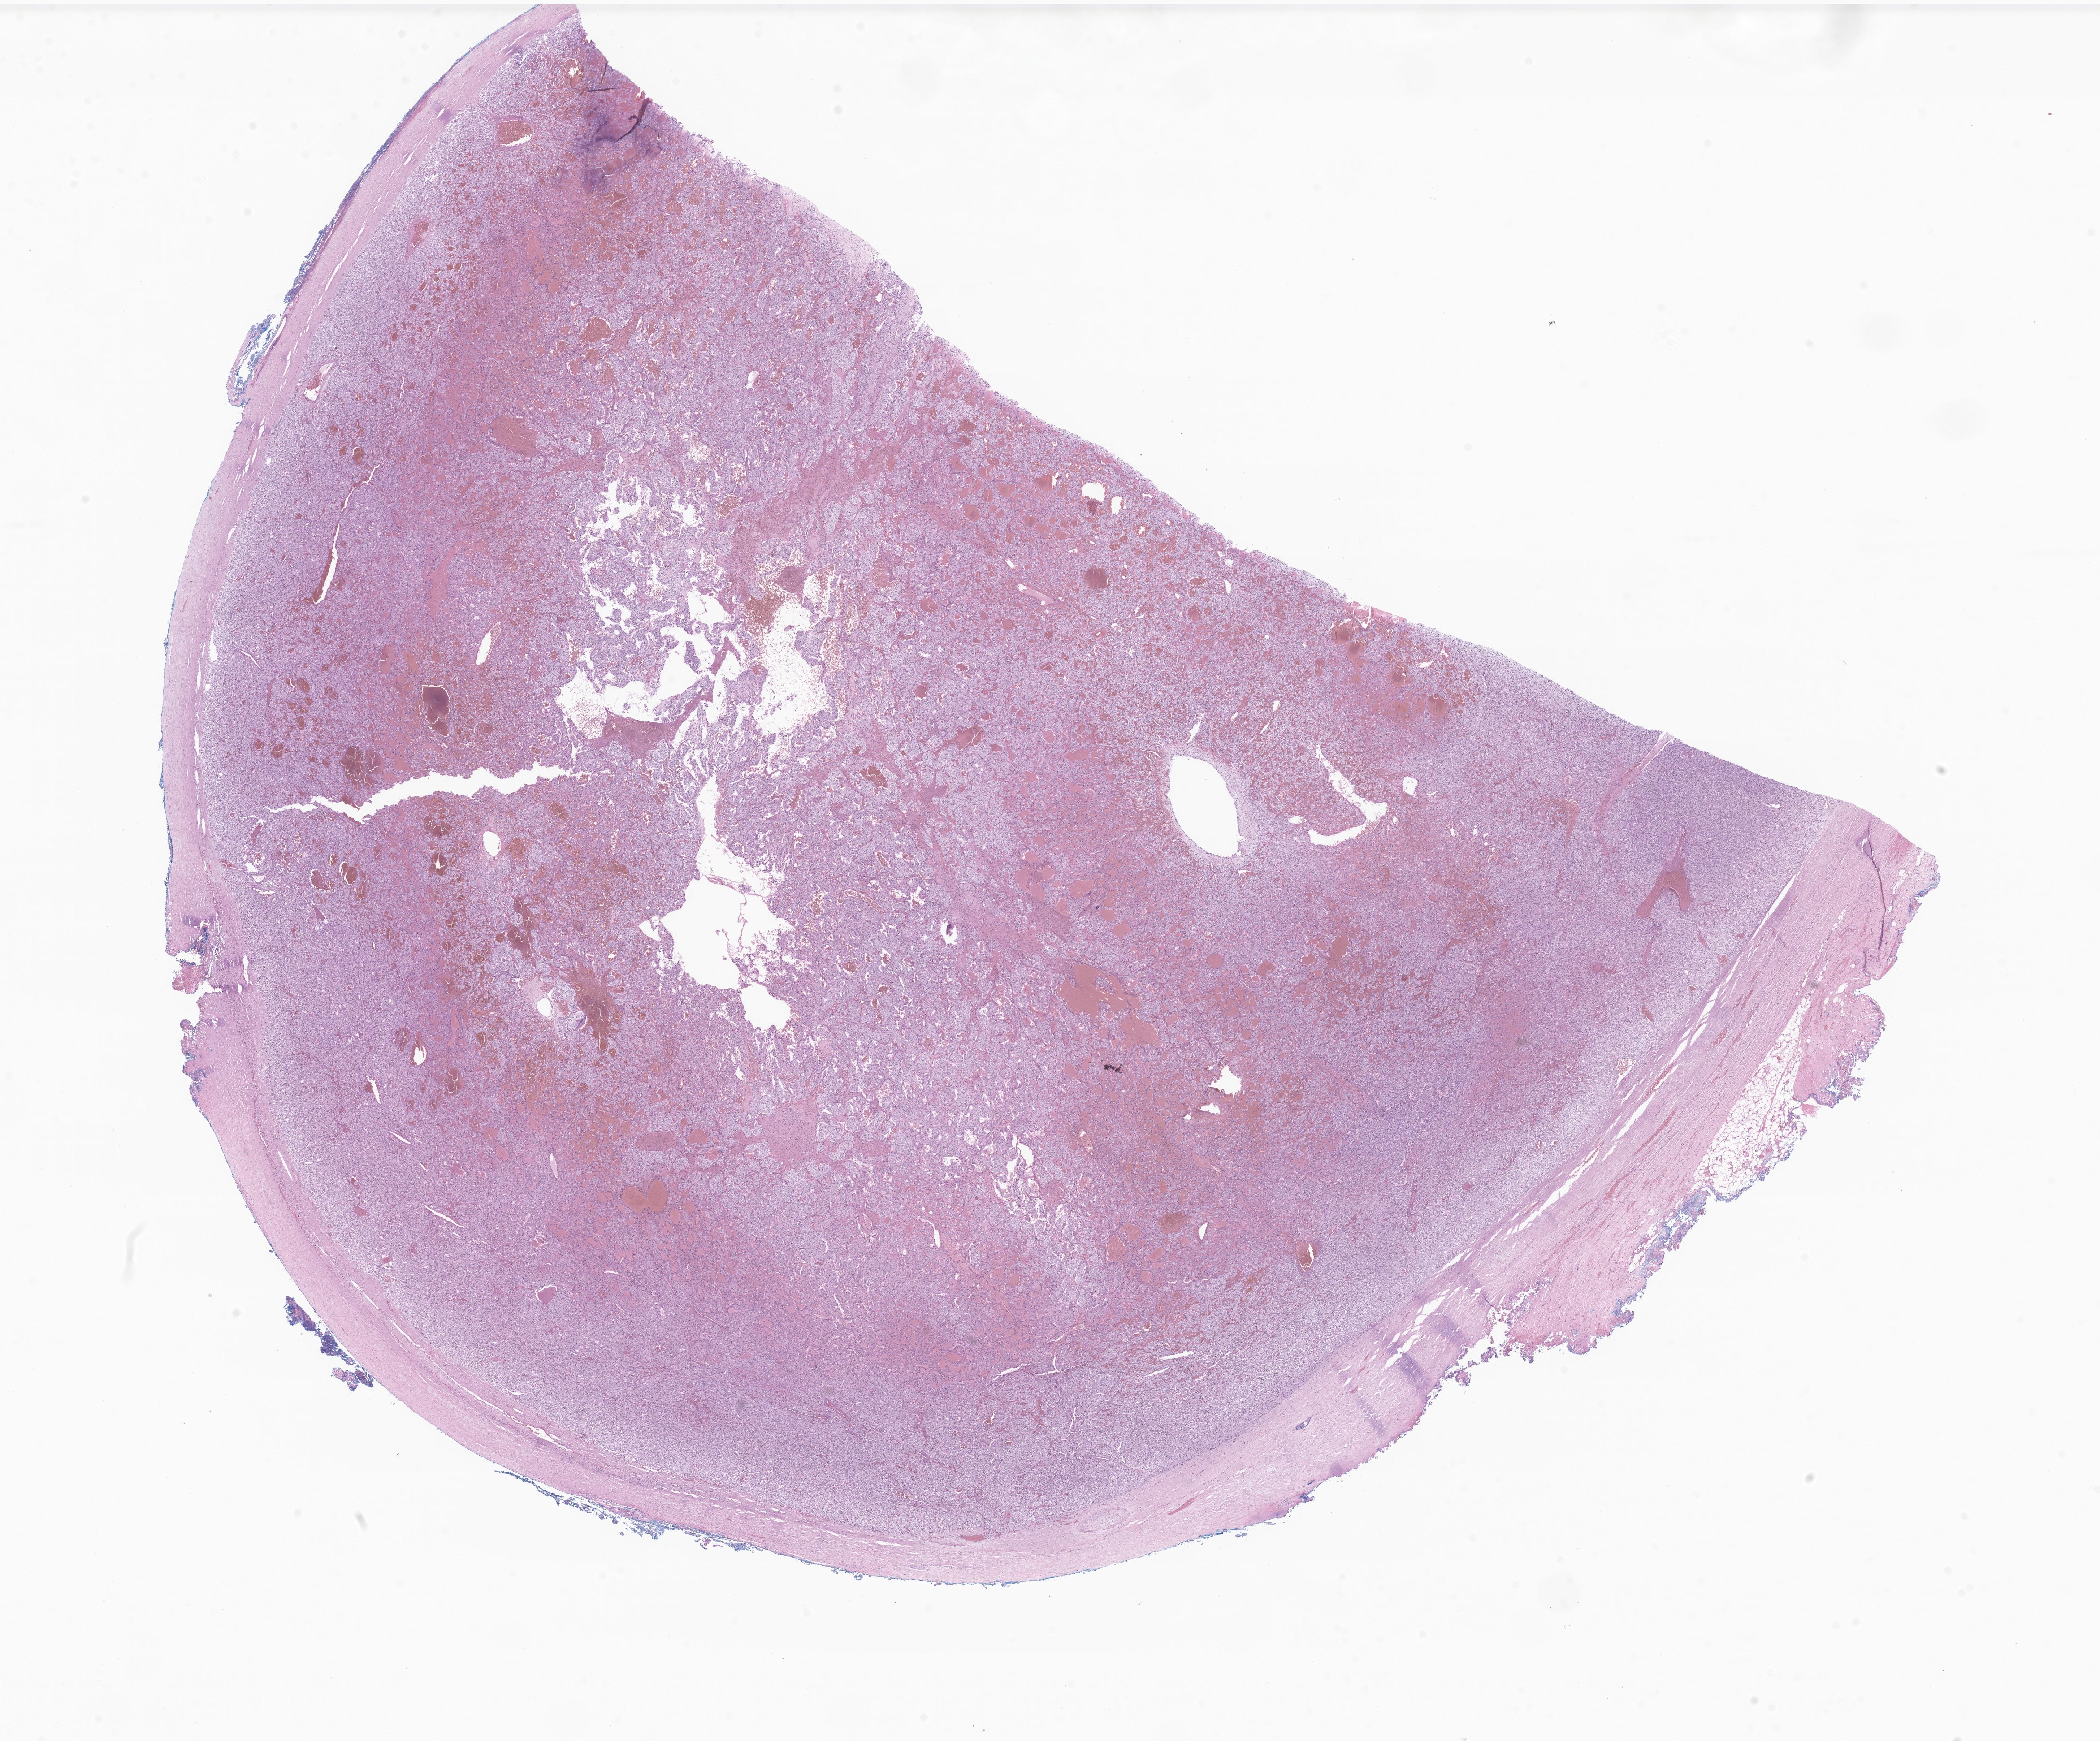
Digitized hematoxylin and eosin (H&E)-stained section of tumor tissue from the adrenal gland — a low-resolution overview of the entire scanned area, about 24.5 x 20.3 mm; FFPE section. Patient: female, age 185 months (15 years 5 months).
Diagnosis (ICD-O-3 morphology term): Pheochromocytoma, NOS.